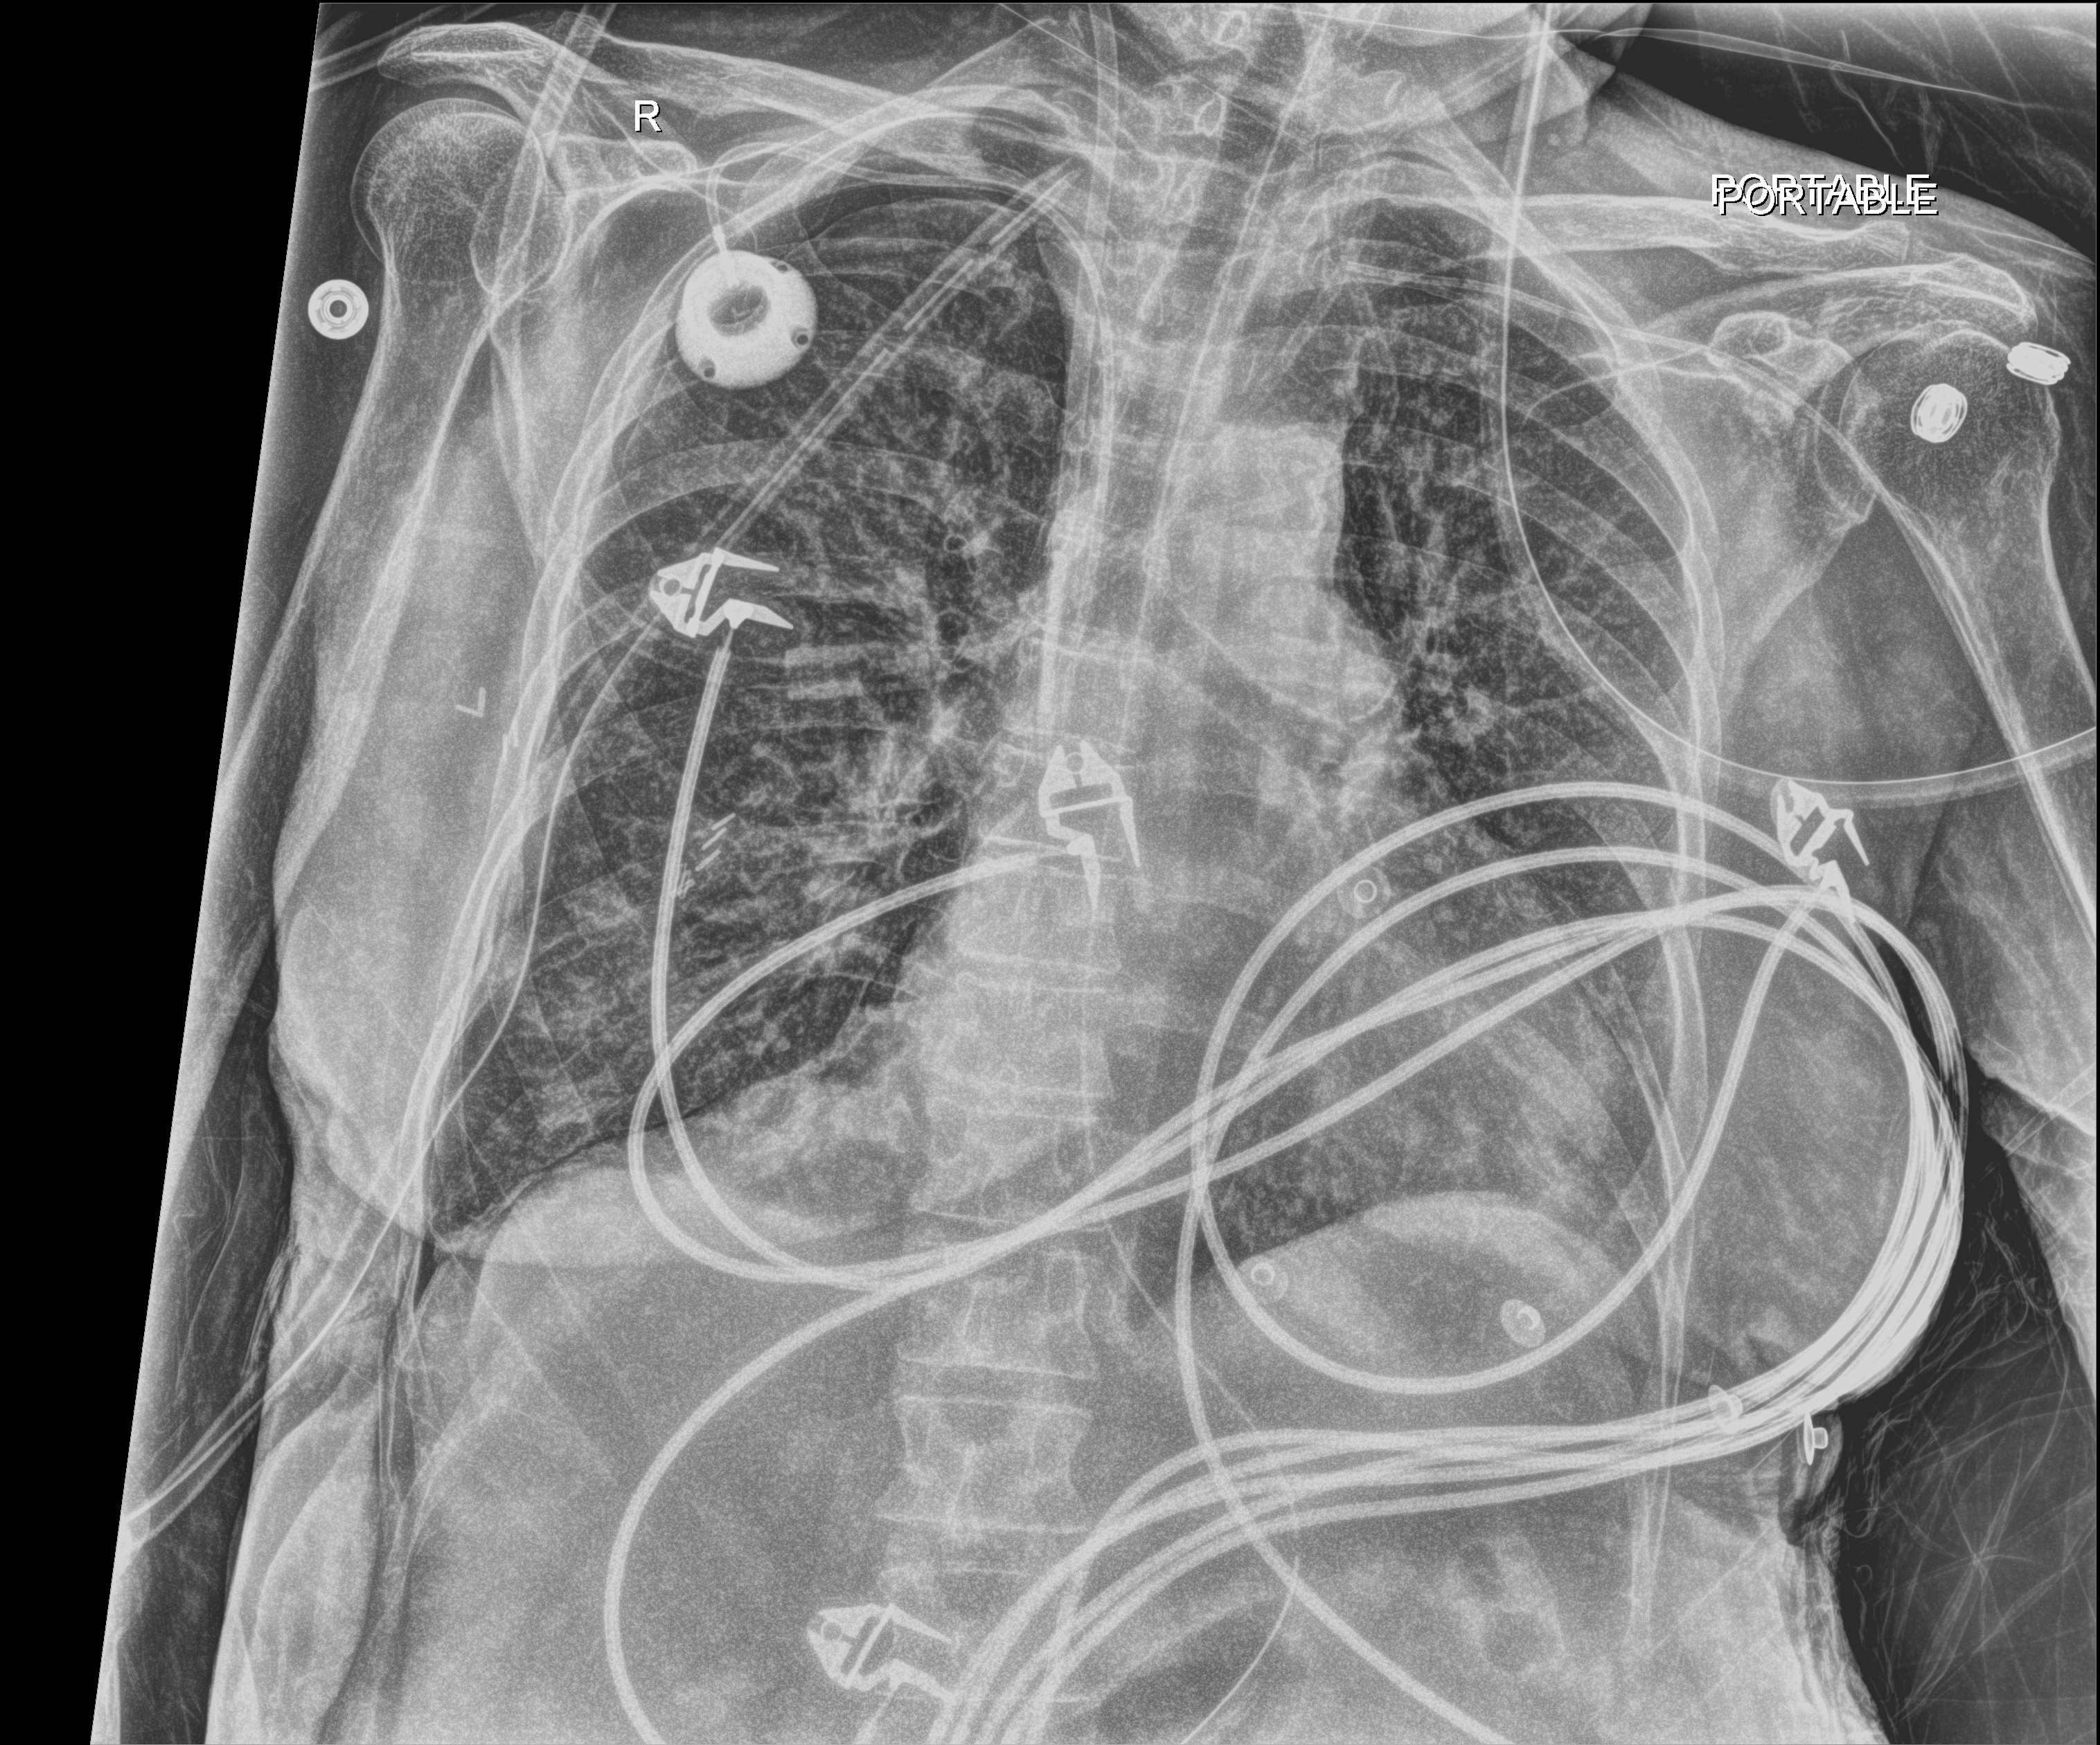
Chest X-ray. Female patient hospitalised with COVID-19, age 60–74 years.
Admission-level facts for this patient (not findings on this image; timing relative to this image not recorded): COPD (admission record): no.